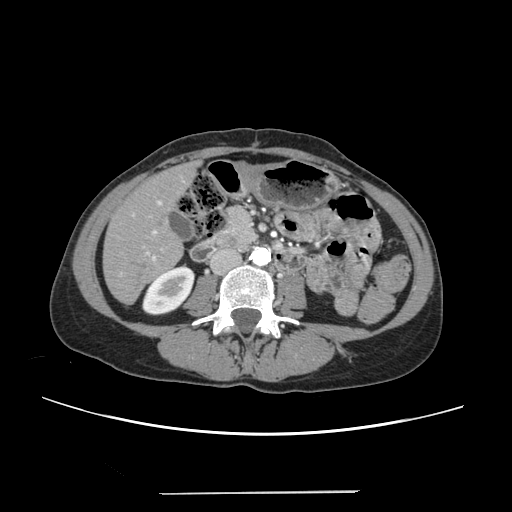
Contrast-enhanced abdominal CT, one axial slice; position 77 of 240 along the scan axis; intravenous contrast given; soft-tissue window (W 400 / L 40 HU); 1.25 mm slice thickness; 512 × 512 image matrix, field of view 371 × 371 mm. Female patient, age 60 years. From the clinical record (not read from this slice): diagnosis: colorectal cancer liver metastases, imaged before liver resection; multiple liver metastases: no; largest metastasis: 1.5 cm; chemotherapy before resection: yes.
Structures marked on this image (expert manual segmentation):
- liver: bounding box <105,165,195,303> (left, top, right, bottom; pixels)
- planned liver remnant (the part of the liver to remain after resection): <105,172,182,303>
- portal vein (with intrahepatic branches): <133,201,163,260>